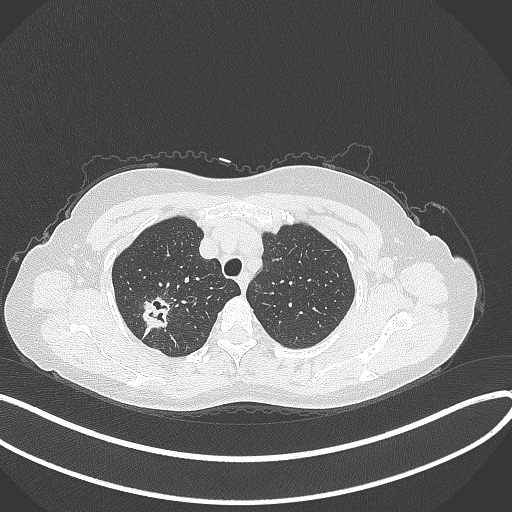
Chest CT, one axial slice. Position 297 of 337 along the scan axis. Reconstruction kernel B70f. Lung window (W 1500 / L -600 HU). 1 mm slice thickness. 512 × 512 image matrix. Patient: female, 50 years. From the clinical record (not read from this slice): clinical TNM (as recorded): T1c N0 M0; histopathological grade: G2-3.
Outlined on this slice (rectangle marked by the reading radiologist):
- lung tumour (recorded histology: adenocarcinoma): bounding box (x1, y1, x2, y2) in pixels: (131, 293, 170, 338)